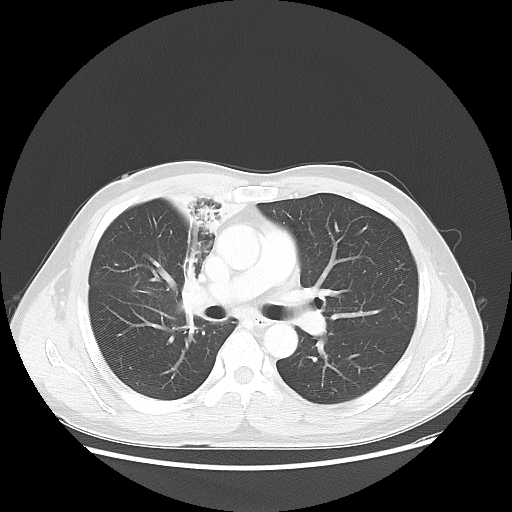
Chest CT, one axial slice; position 32 of 56 along the scan axis; 100 kVp; lung window (W 1500 / L -600 HU); 5 mm slice thickness; 512 × 512 image matrix. Male patient, age 60 years. Case-level facts recorded for this patient, not image findings: clinical TNM (as recorded): T2a N1 M0.
Structures marked on this image (bounding box drawn by a radiologist):
- lung tumour (recorded histology: squamous cell carcinoma): bounding box <154,179,253,249> (left, top, right, bottom; pixels)